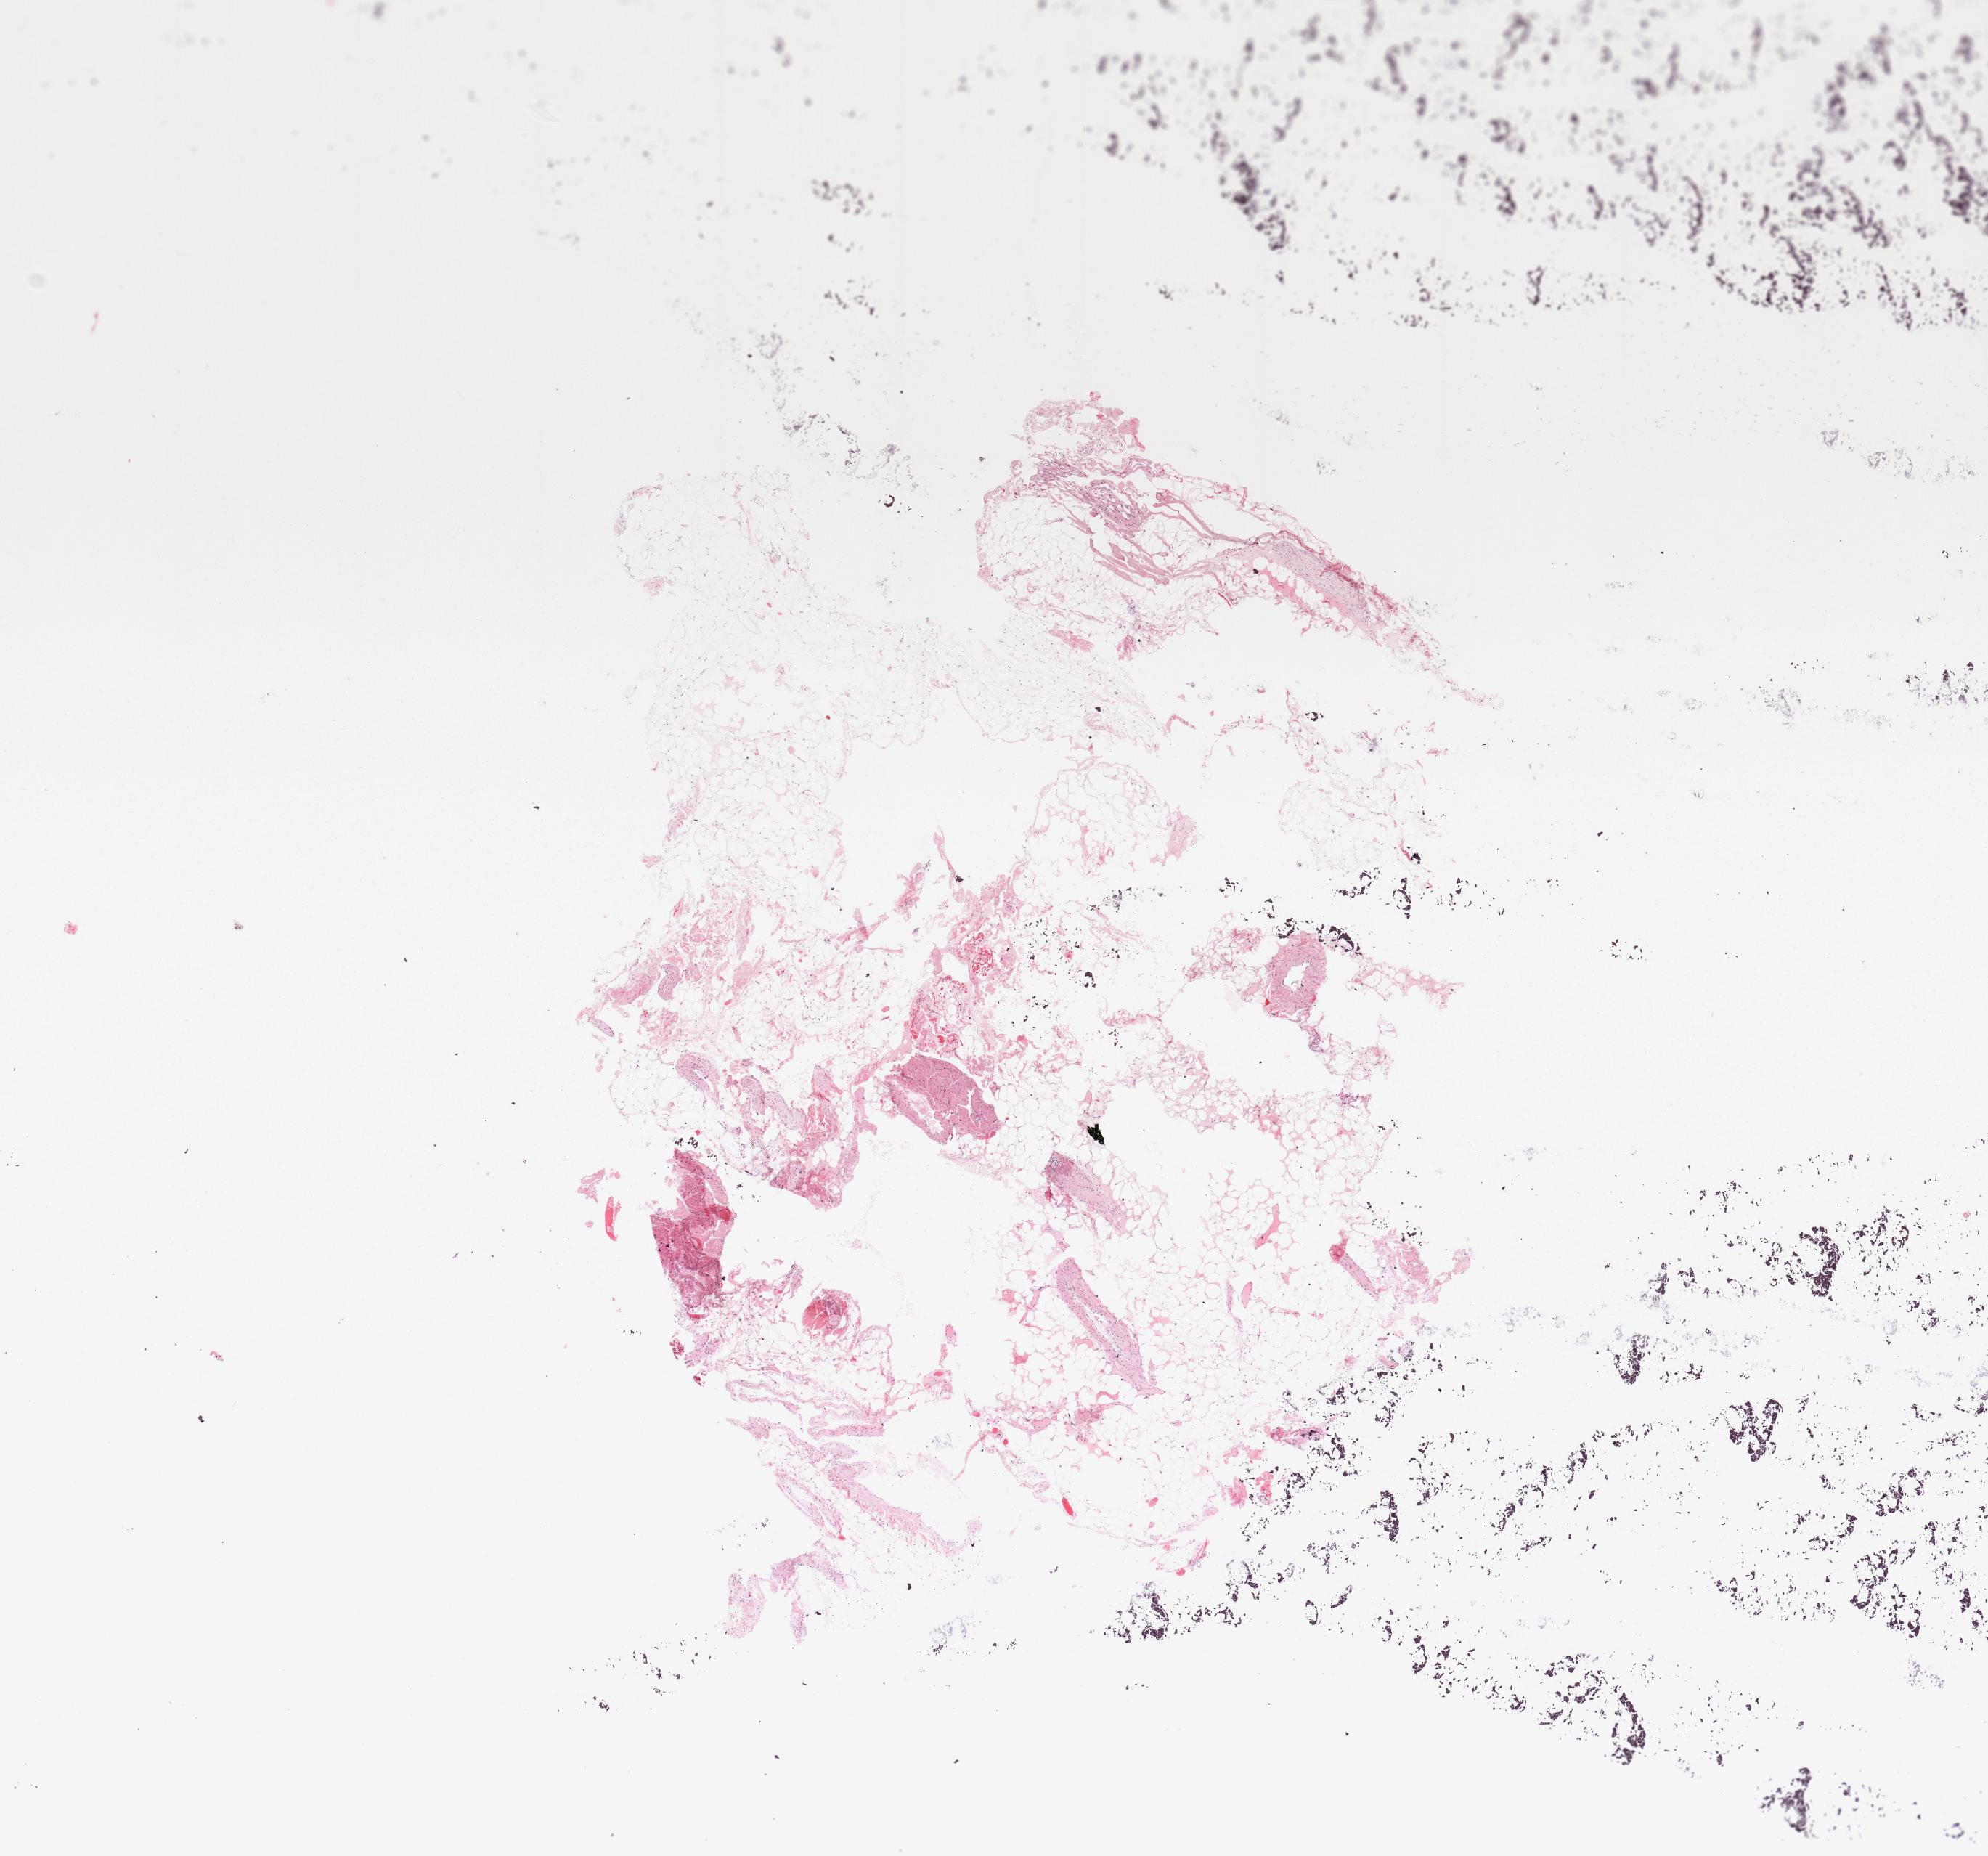
Whole-slide histology image, H&E-stained, whole scanned area (about 10.8 x 10.1 mm) shown as a low-resolution overview, normal (non-tumour) tissue sample, pancreas. Male, 64 y/o.
- this section: normal (non-tumour) tissue from the same patient
- patient diagnosis: Infiltrating duct carcinoma, NOS